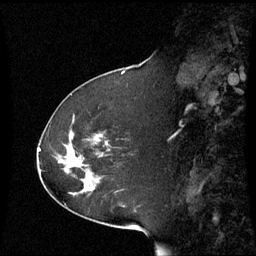
Breast MRI (dynamic contrast-enhanced), one sagittal slice. Slice 24 of 60 in the series (ordered by position). Dynamic contrast-enhanced series, image 2 of 3 at this slice position (ordered by acquisition). 1.5 T. TE 4.2 ms, TR 8.9 ms. 256 × 256 image matrix, field of view 230 × 230 mm. Female patient, age 51 years. From the clinical record (not read from this slice): setting: breast cancer imaged before/during neoadjuvant chemotherapy; receptor status: HR-positive, HER2-negative.
Outlined on this slice (semi-automatic segmentation, software-assisted and operator-edited):
- analysis volume of interest (the breast-tissue region the enhancement analysis was run in; not a lesion): bounding box <42,121,110,199> (left, top, right, bottom; pixels)
- tumour enhancement mask (voxels above the 70 % enhancement threshold inside the analysis volume of interest): <70,156,72,158>